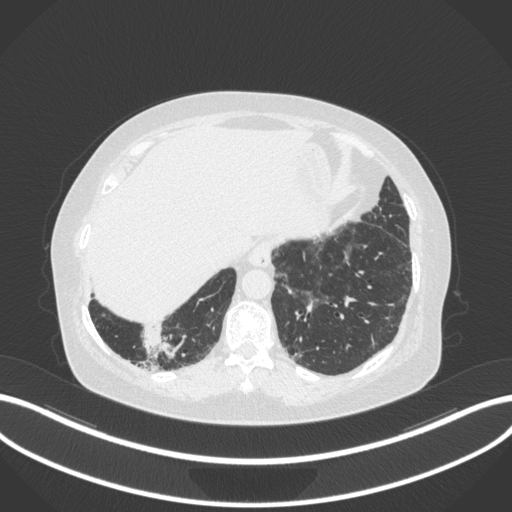
Chest CT, one axial slice. Slice 21 of 303 in the series (ordered by position). Reconstruction kernel B31f. Lung window (W 1500 / L -600 HU). 1 mm slice thickness. 512 × 512 image matrix, field of view 400 × 400 mm. Female patient, age 65 years. From the clinical record (not read from this slice): clinical TNM (as recorded): T2b N1 M0.
Annotated regions visible in this slice (bounding box drawn by a radiologist):
- lung tumour (recorded histology: adenocarcinoma): bounding box (x1, y1, x2, y2) in pixels: (135, 326, 178, 361)